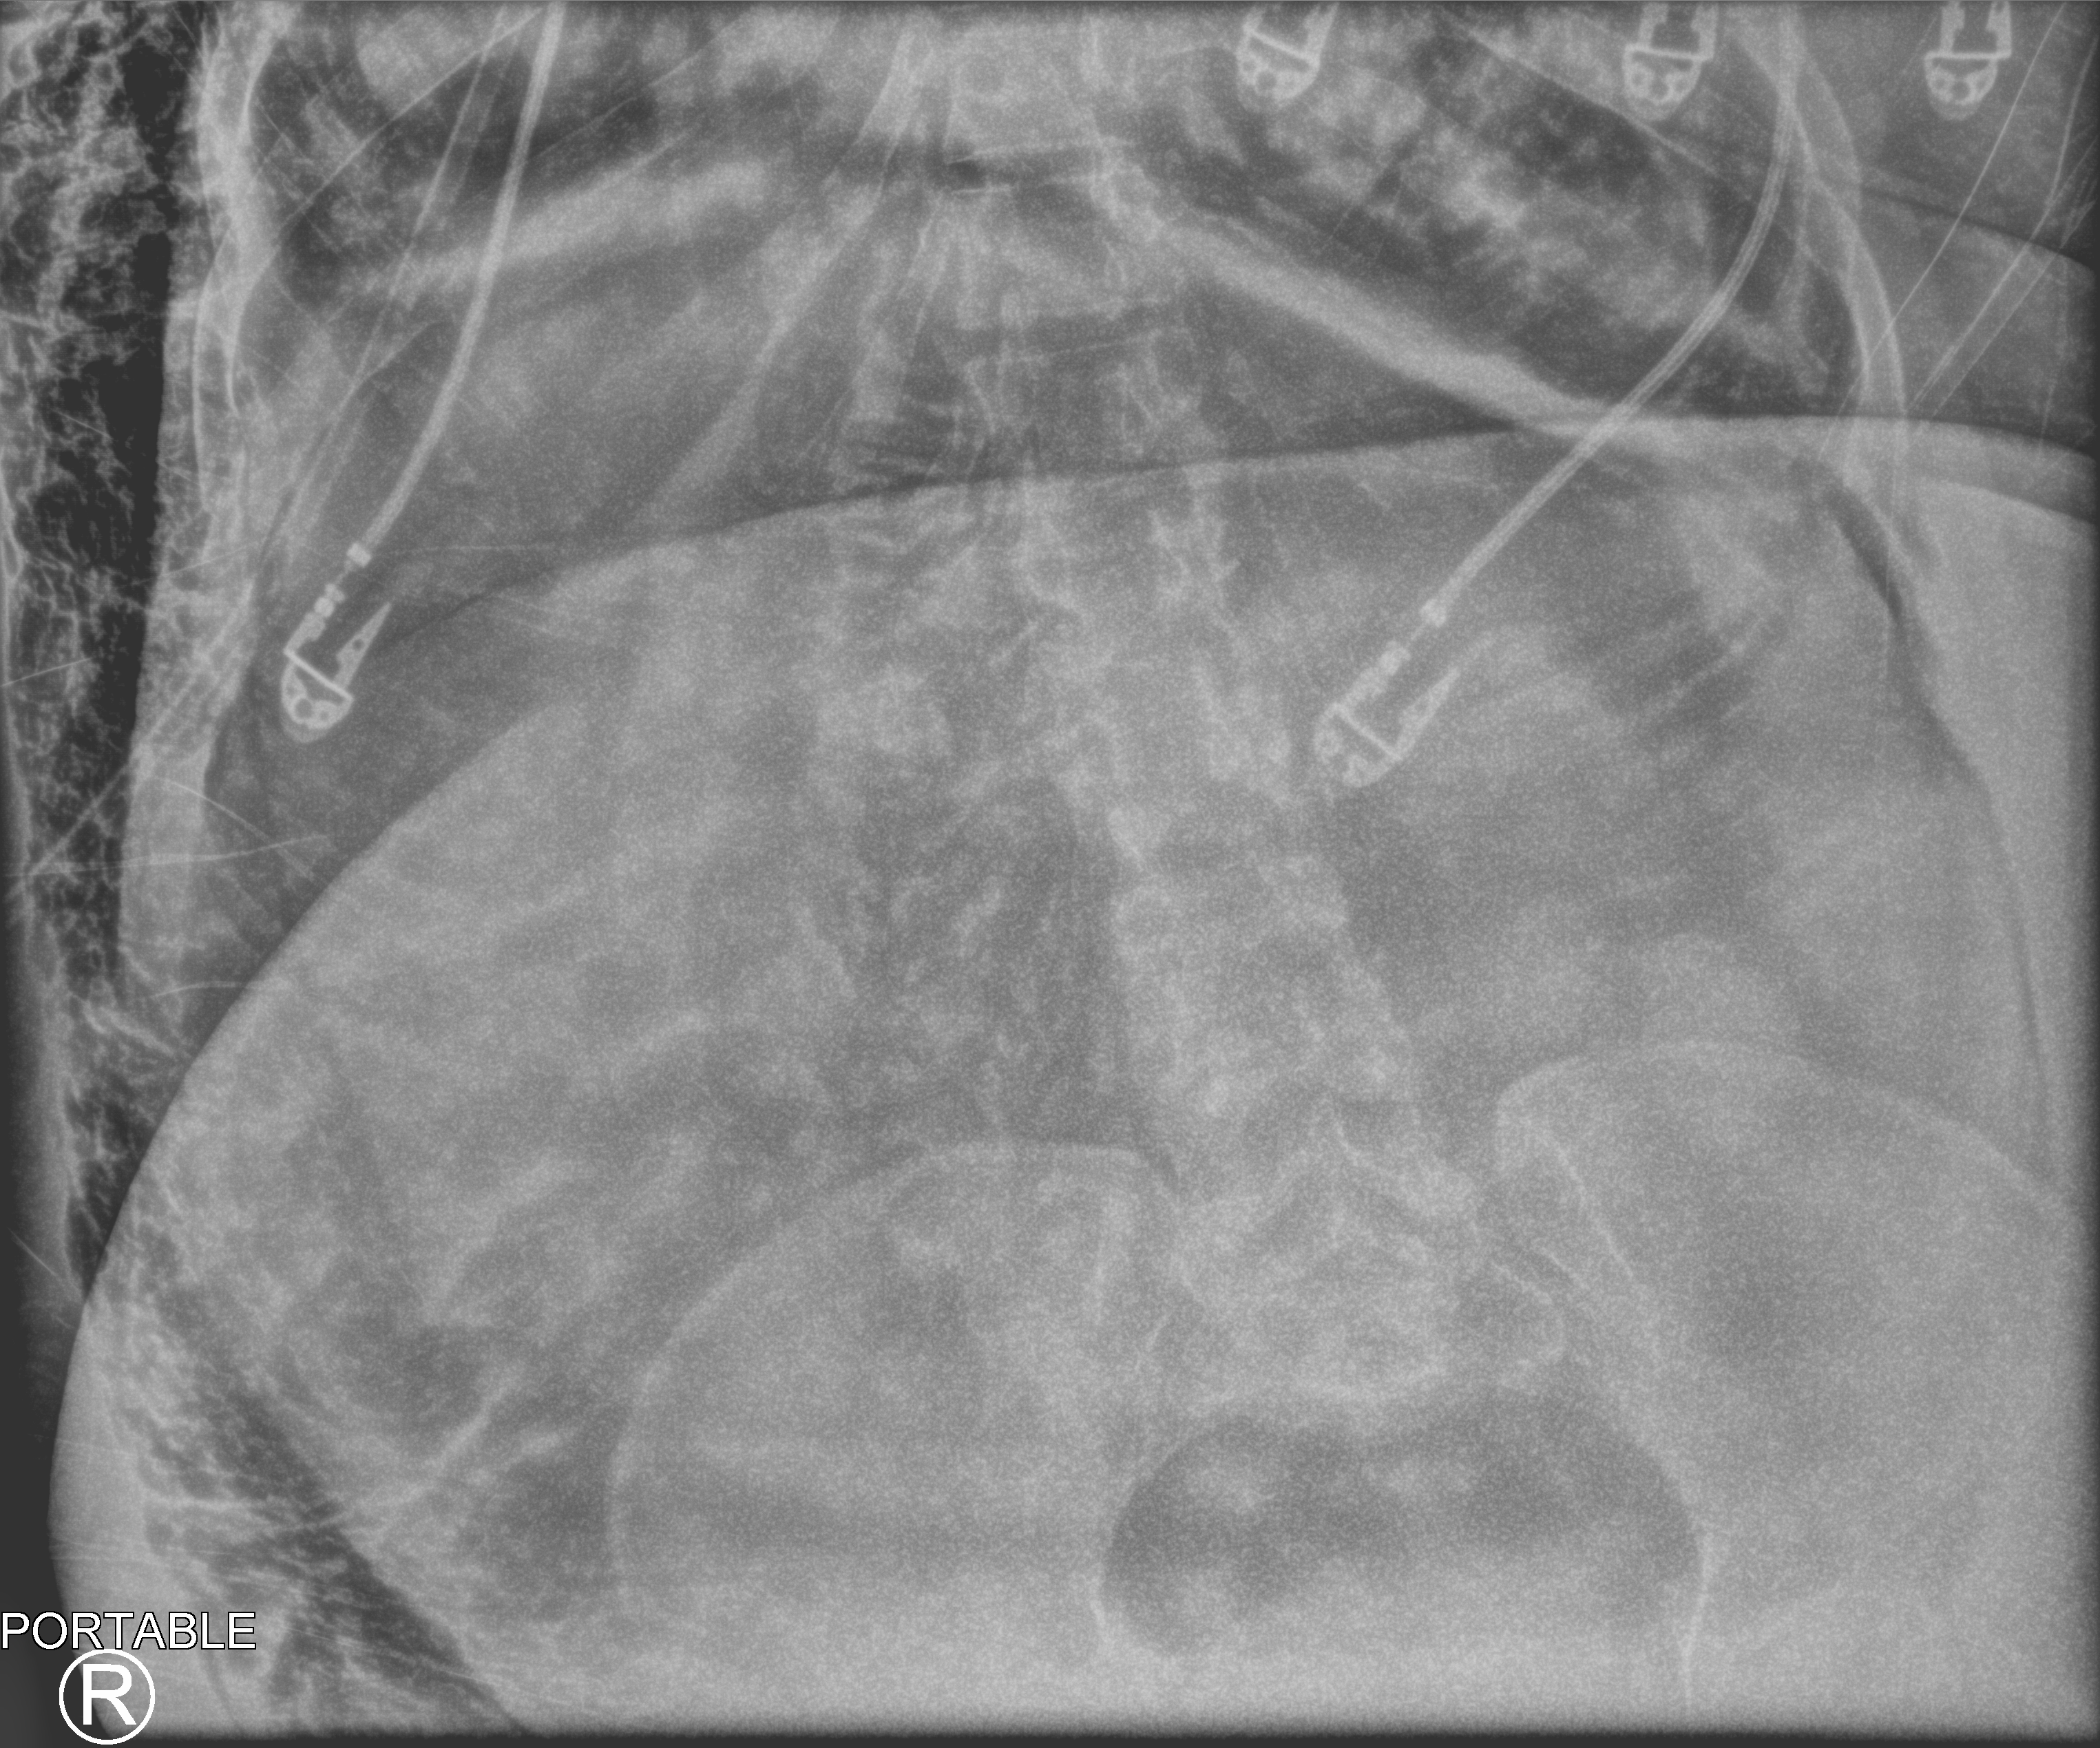
Abdomen X-ray (portable); anteroposterior (AP) projection. Patient hospitalised with COVID-19, aged 18–59 years.
From the hospital-stay record, not from the radiograph (when in the stay this image was taken is not recorded):
- mechanically ventilated during this hospital stay: yes